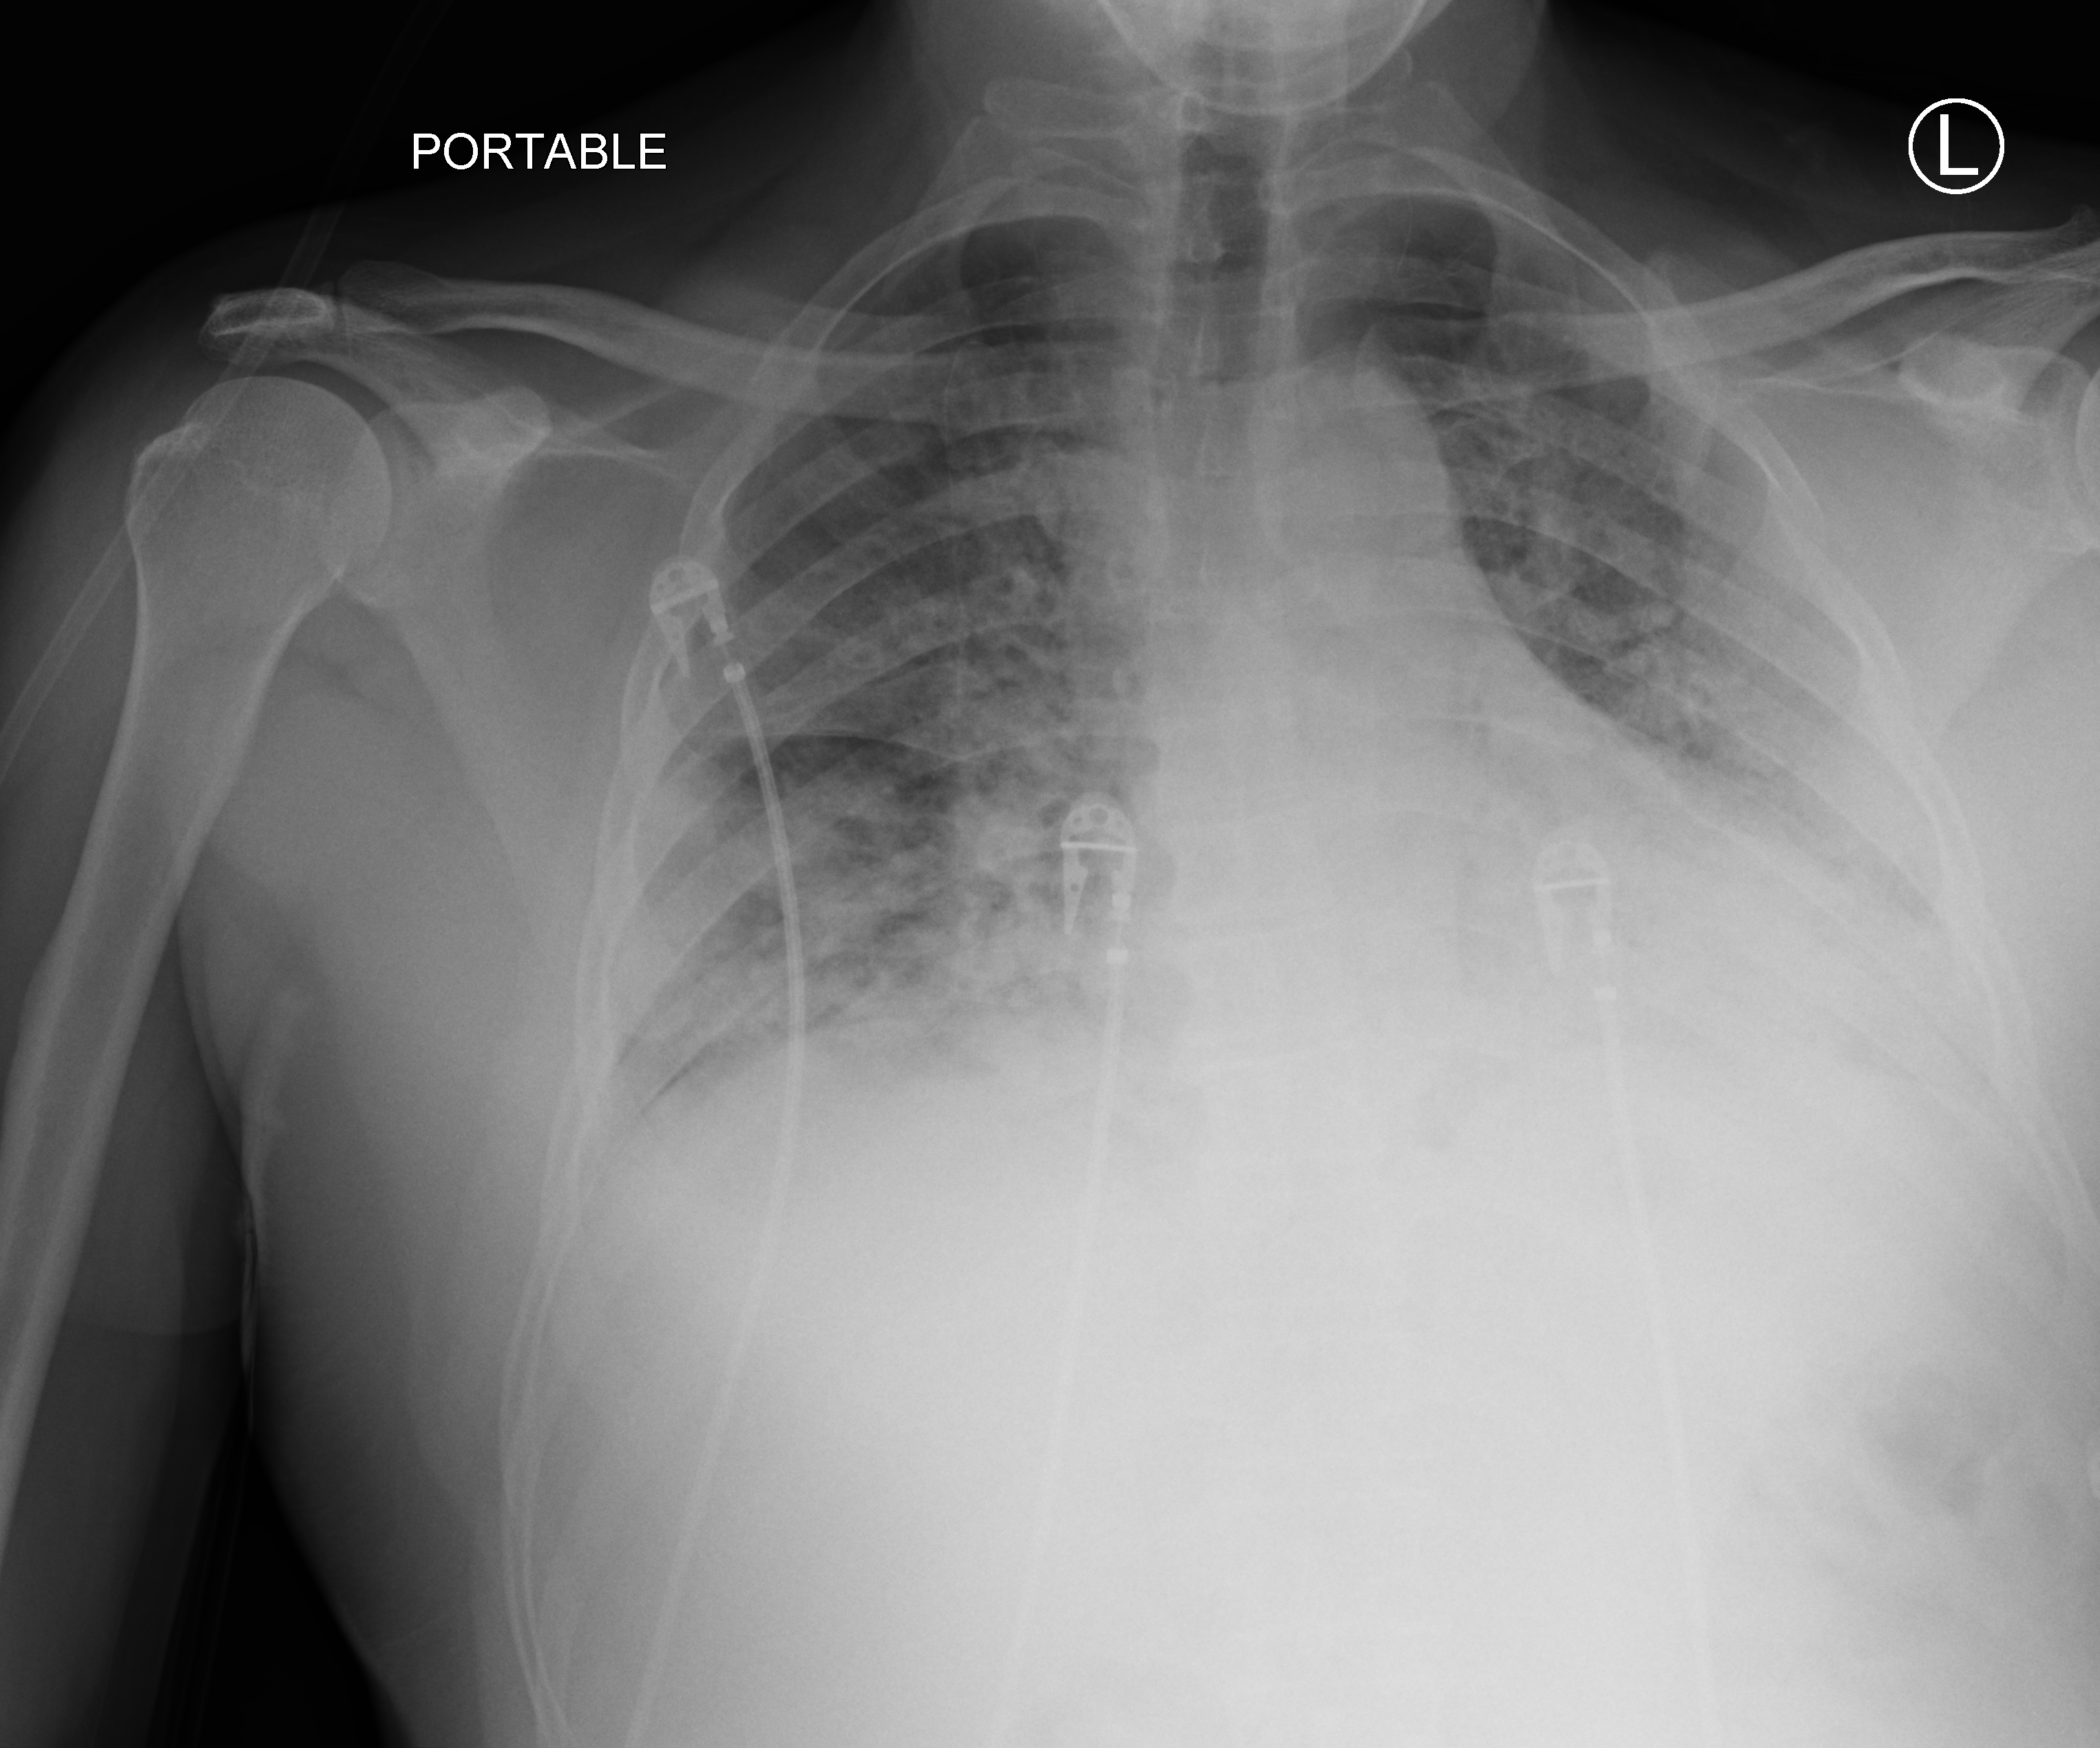
Chest X-ray (portable), anteroposterior (AP) projection. Patient hospitalised with COVID-19; male, aged 18–59 years.
From the hospital-stay record, not from the radiograph (when in the stay this image was taken is not recorded):
- smoking status (admission record): never